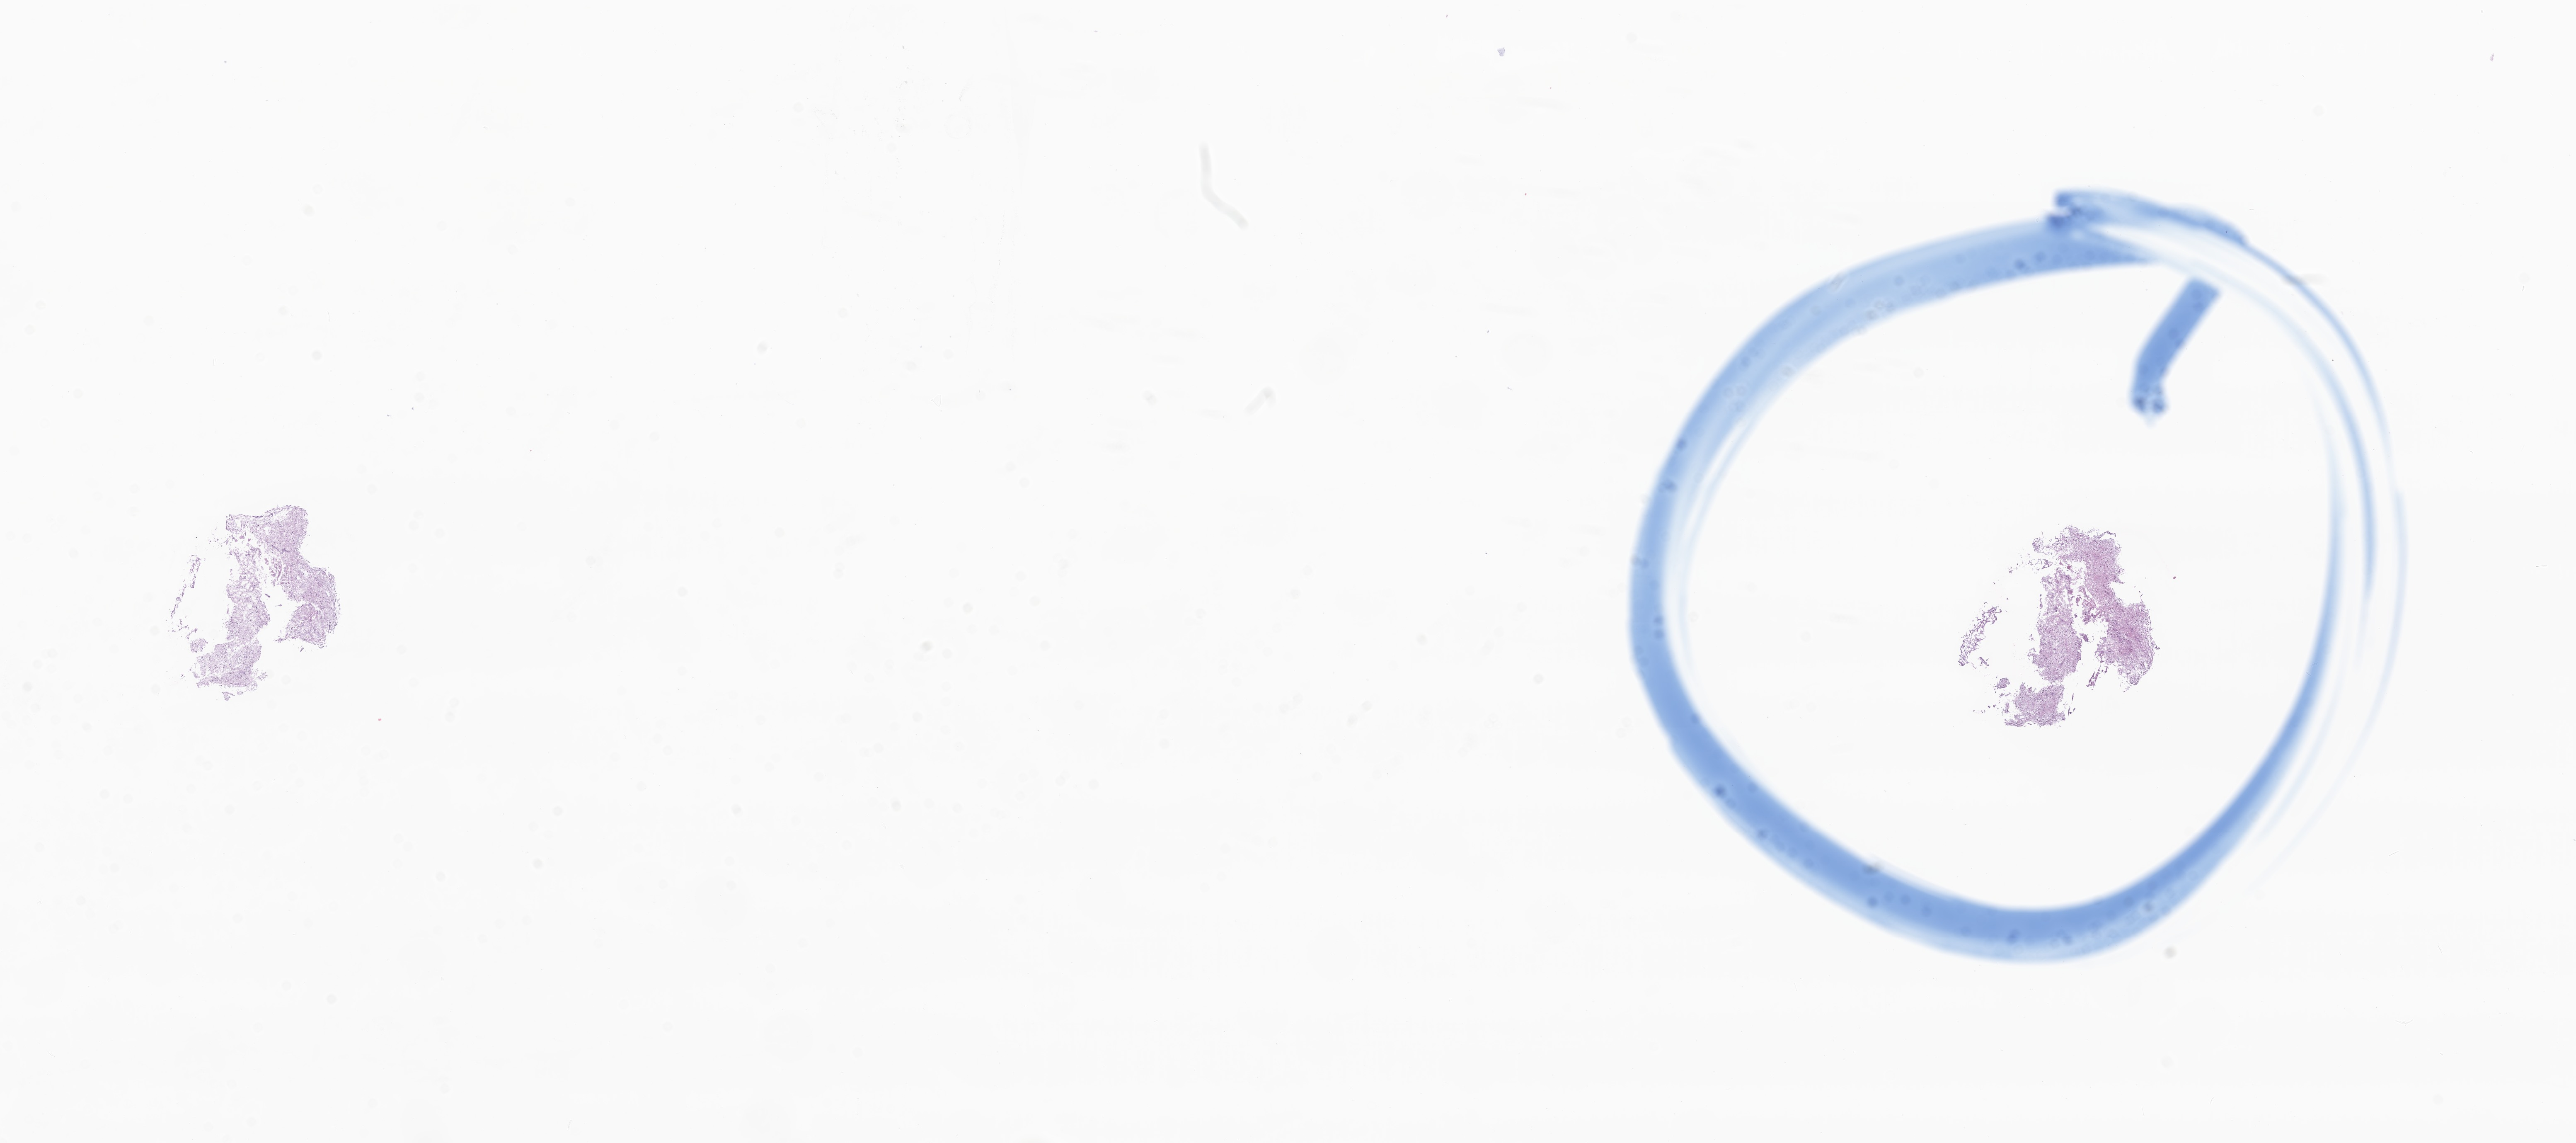
Whole-slide image, hematoxylin and eosin (H&E) stain of tumor tissue from the brain stem — whole scanned area (about 26.2 x 11.6 mm) shown as a low-resolution overview; frozen section. Patient: female, age 57 months (4 years 9 months).
Diagnosis: Pilocytic astrocytoma.